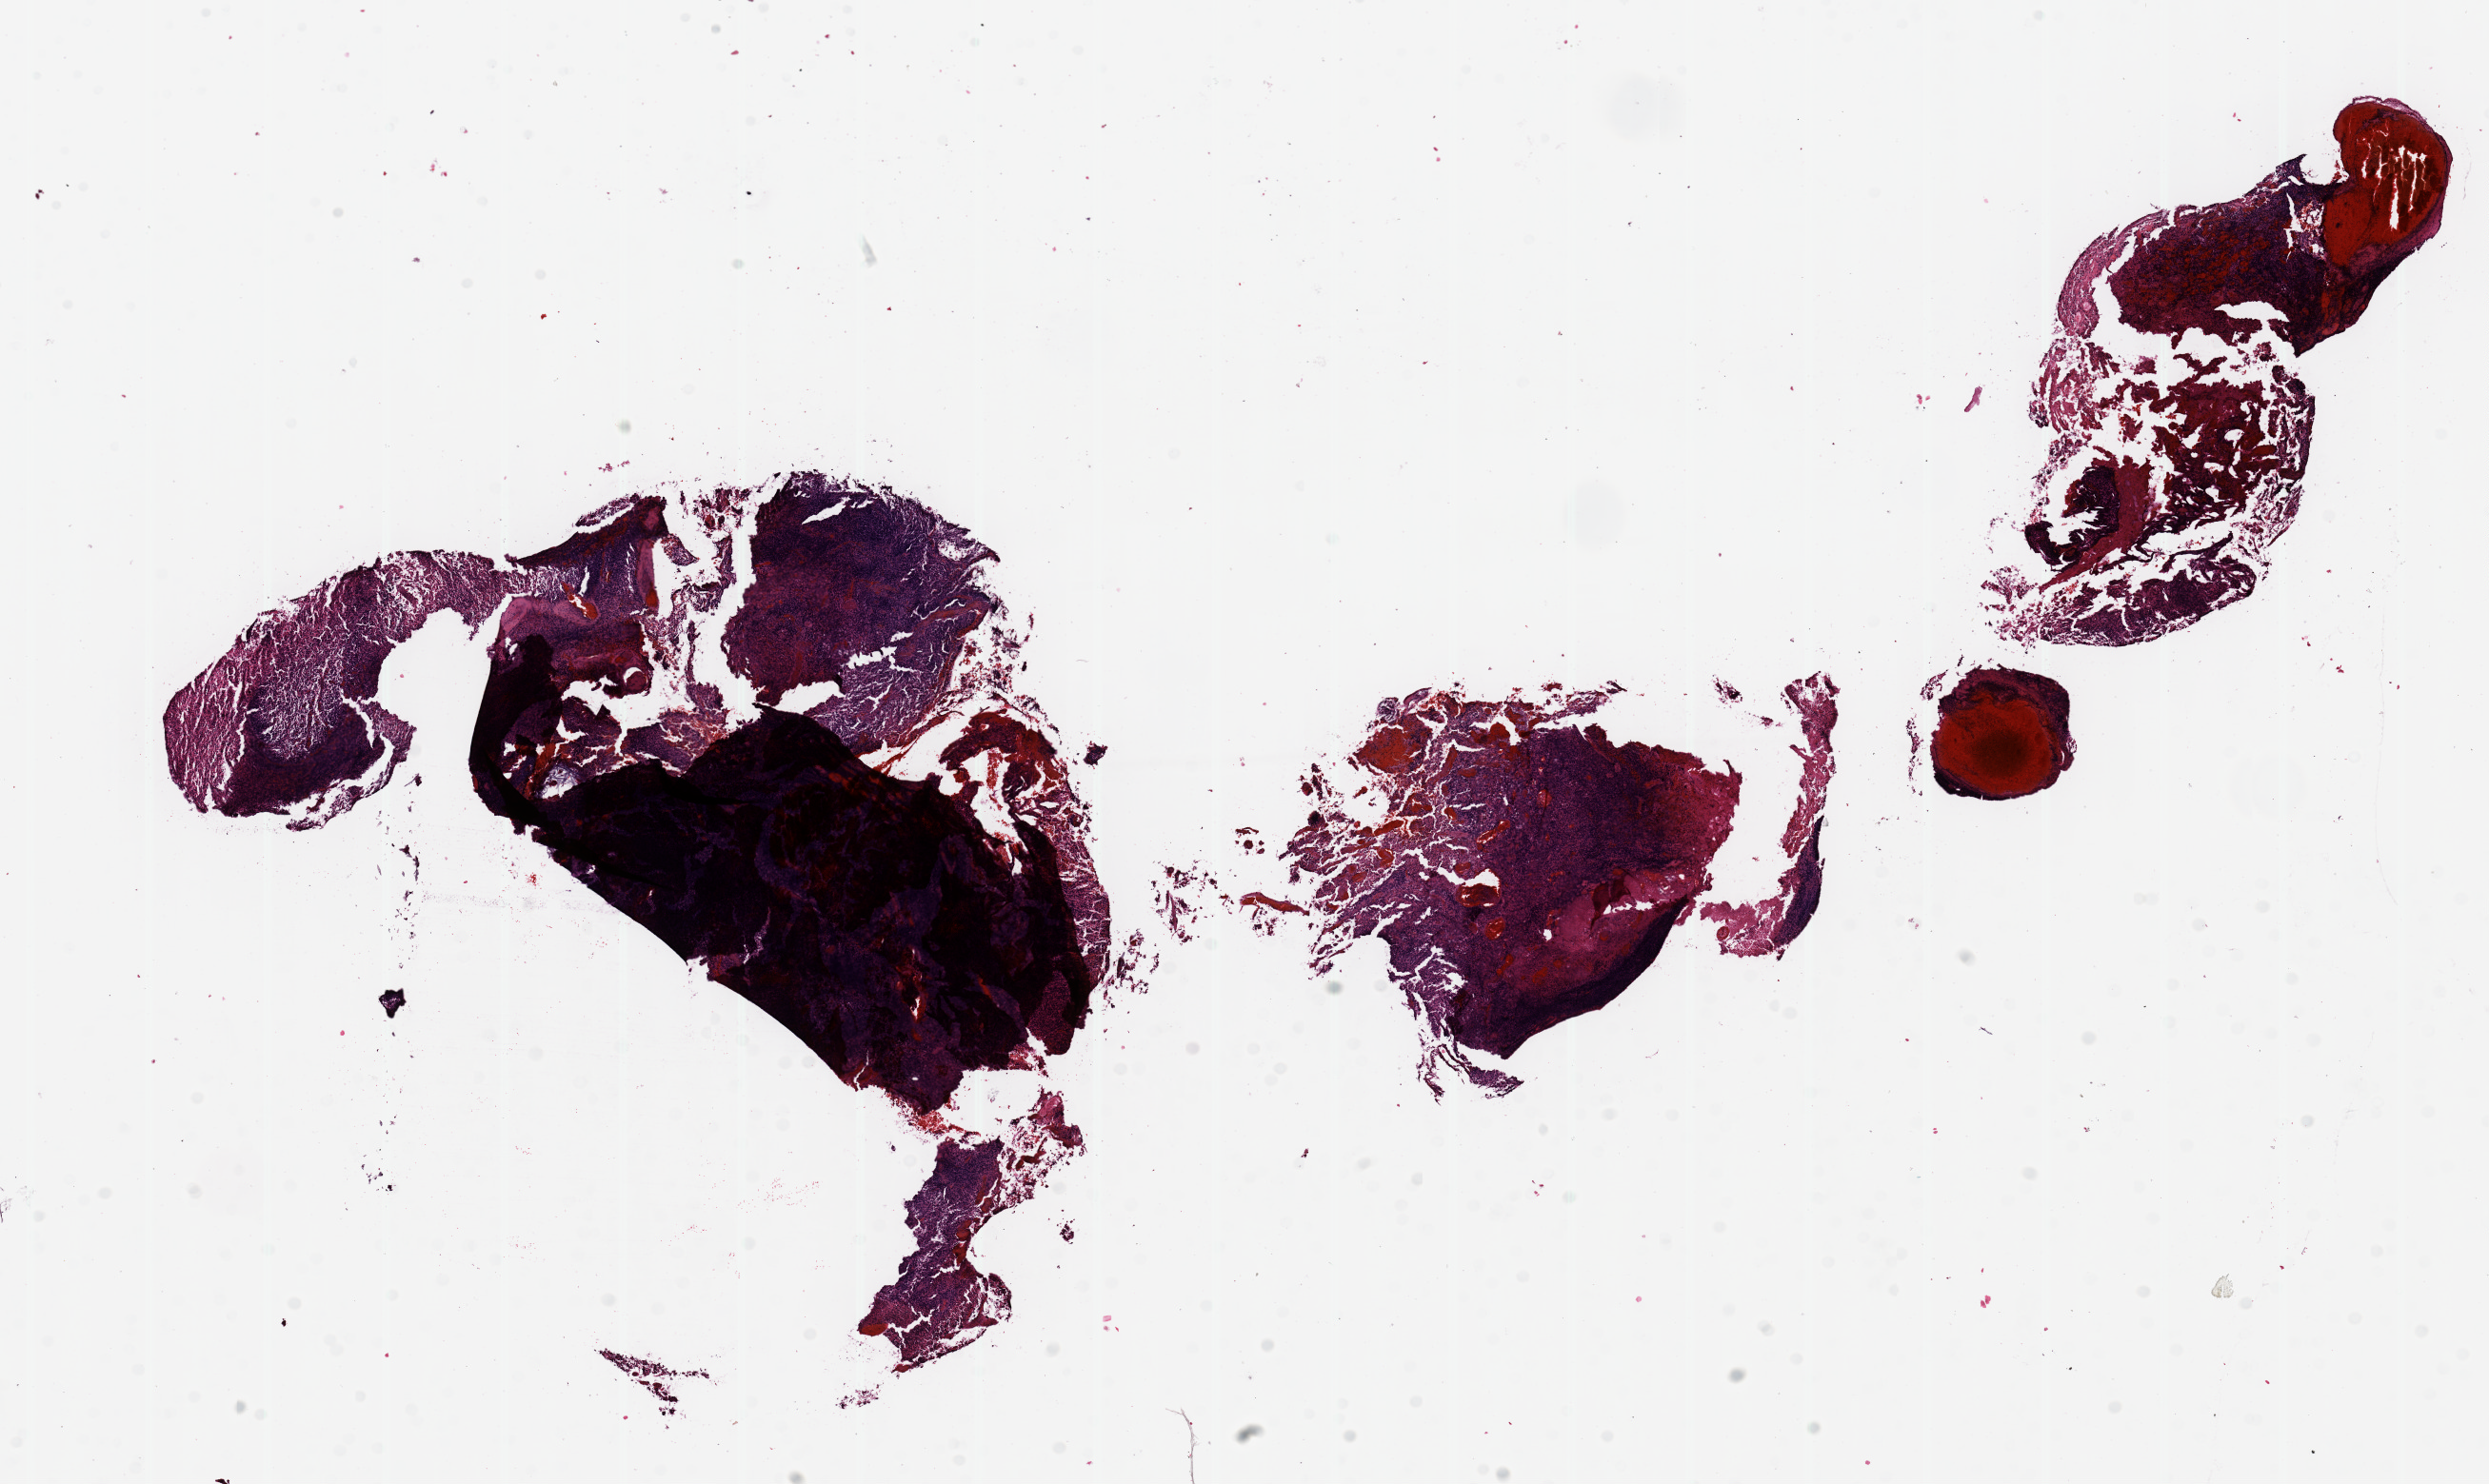
Digitized Hematoxylin and eosin (H&E) stained tissue section (whole slide), a low-resolution overview of the entire scanned area, about 20.7 x 12.3 mm (acquisition: 20x scan); brain, tumour tissue. 70-year-old male patient.
Histologic diagnosis: Glioblastoma. Primary tumour site (as recorded): parietal lobe.